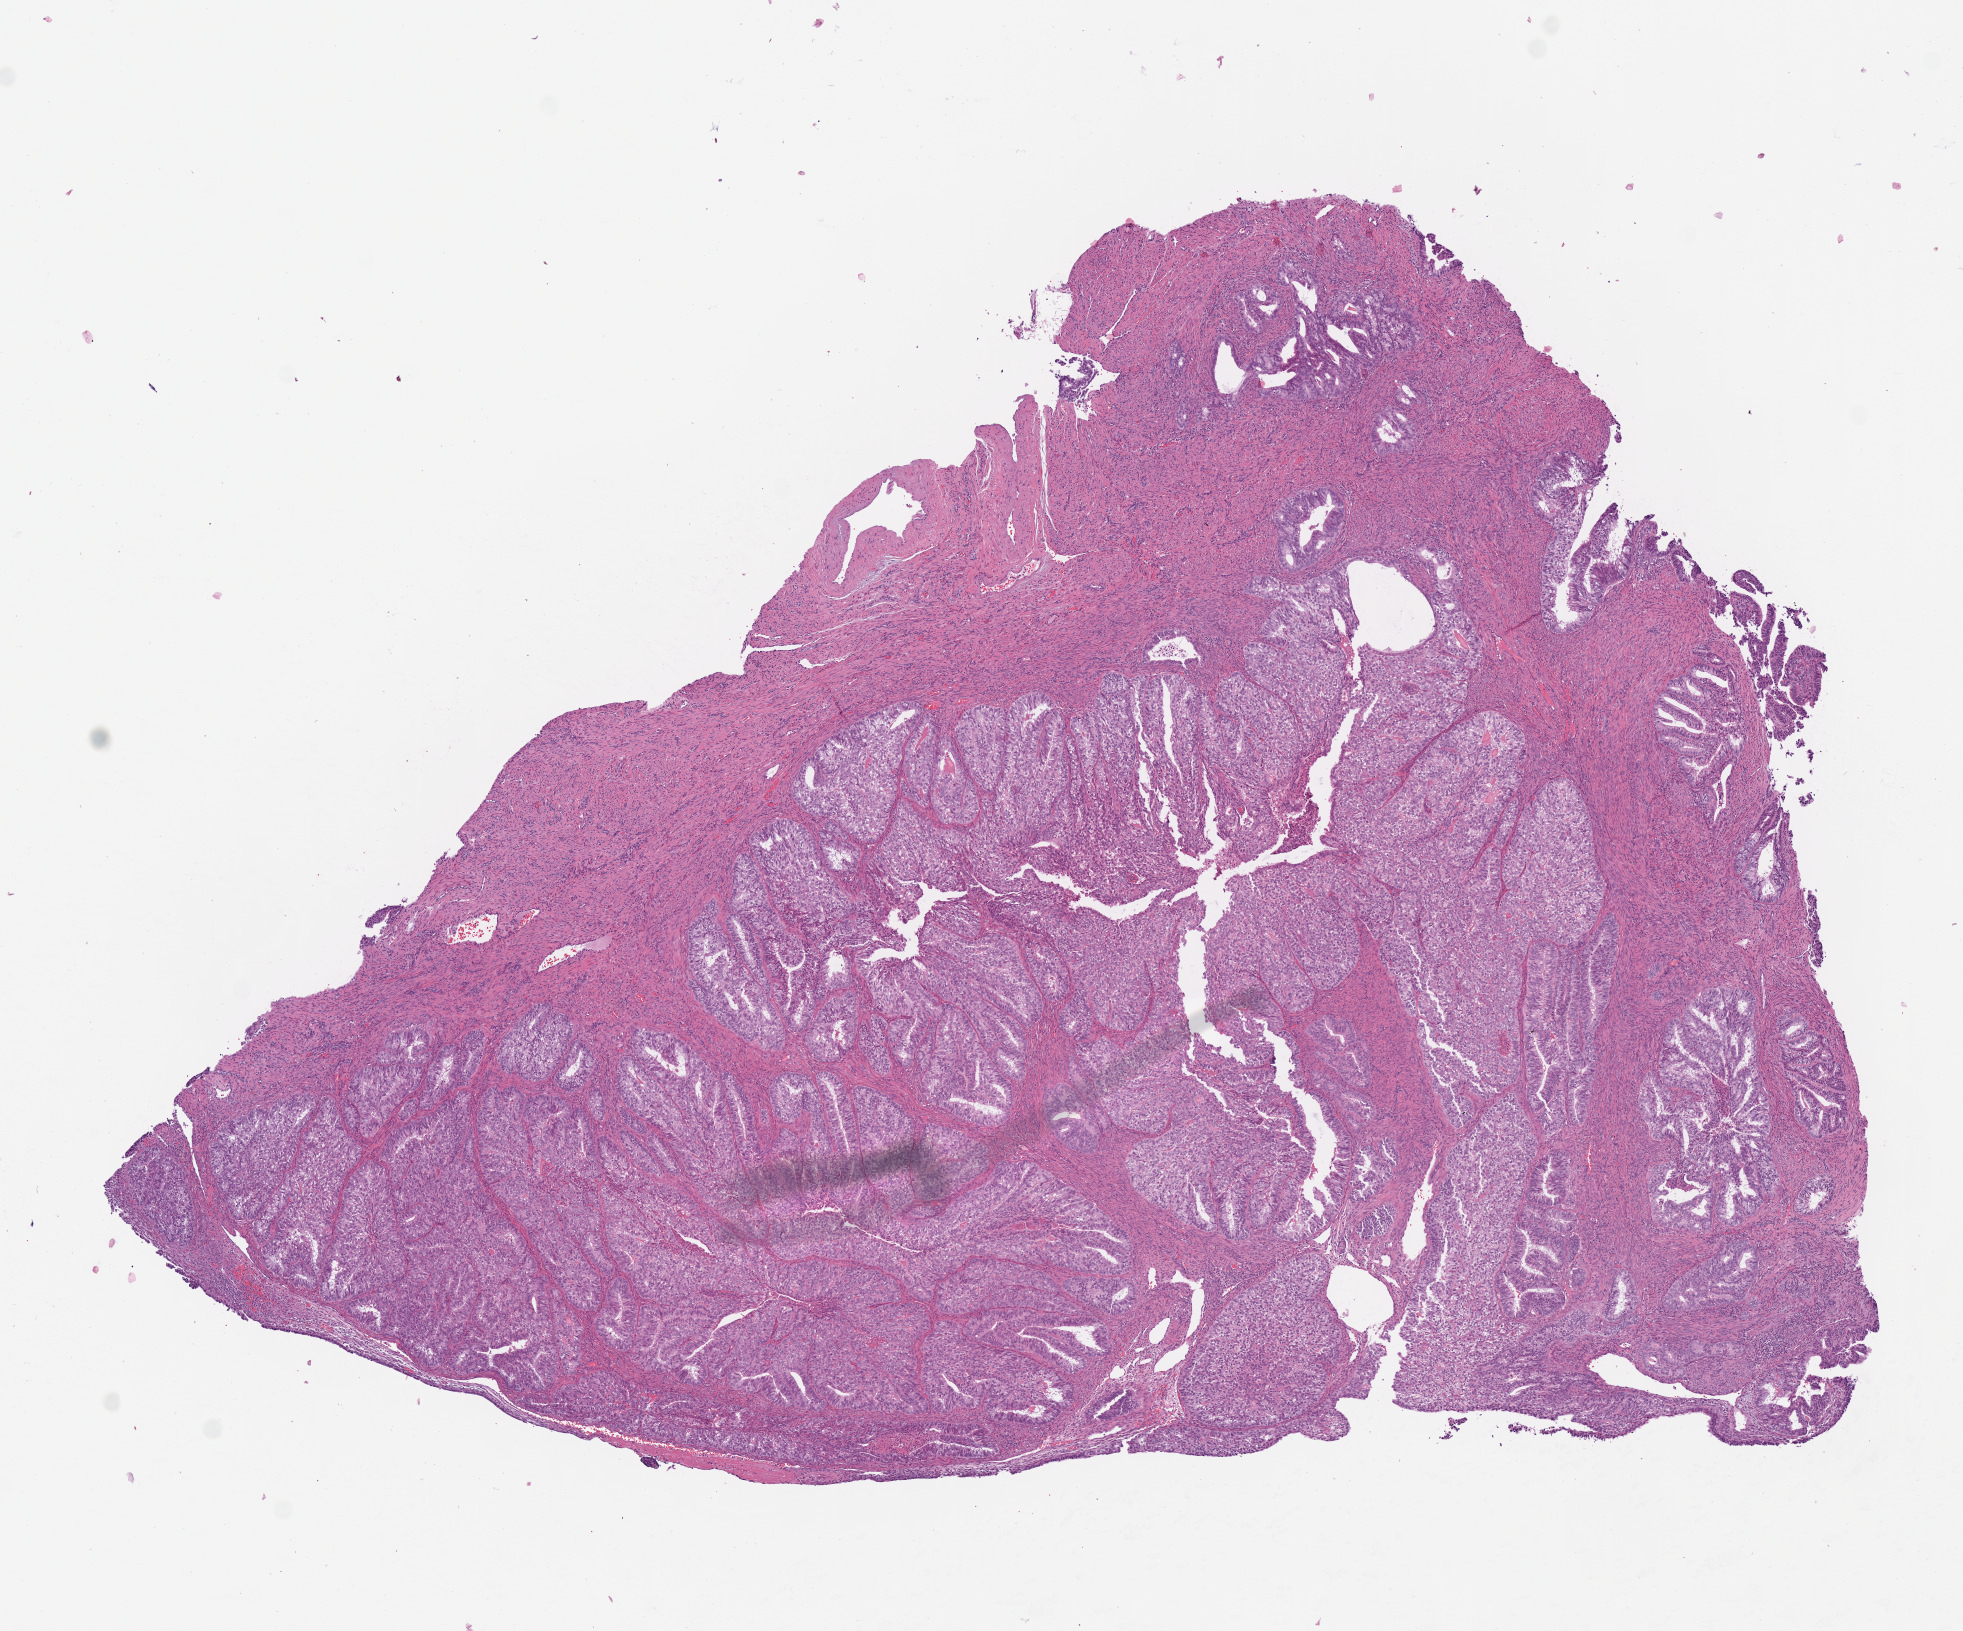
Digitized H&E-stained tissue section (whole slide) — whole scanned area (about 7.7 x 6.4 mm) shown as a low-resolution overview; formalin-fixed paraffin-embedded (FFPE) diagnostic section; primary tumour sample from the uterus. Patient: female, age at initial diagnosis 60 years. Histologic grade: G3 (poorly differentiated).
FIGO stage: II. Diagnosis: Endometrioid adenocarcinoma, NOS (endometrium).